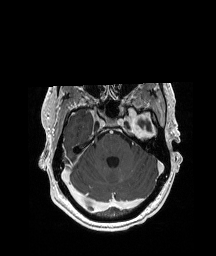
Brain MRI from a brain-tumour surgery series, one axial slice; position 141 of 208 along the scan axis; T1-weighted post-contrast; 1 mm slice thickness; 216 × 256 image matrix, field of view 228 × 270 mm. Case-level facts recorded for this patient, not image findings: histopathology: Glioblastoma; WHO grade: 4; IDH mutation: no.
Structures marked on this image (expert manual segmentation):
- previous resection cavity: bounding box <137,120,152,132> (left, top, right, bottom; pixels)
- tumour: <123,103,158,135>